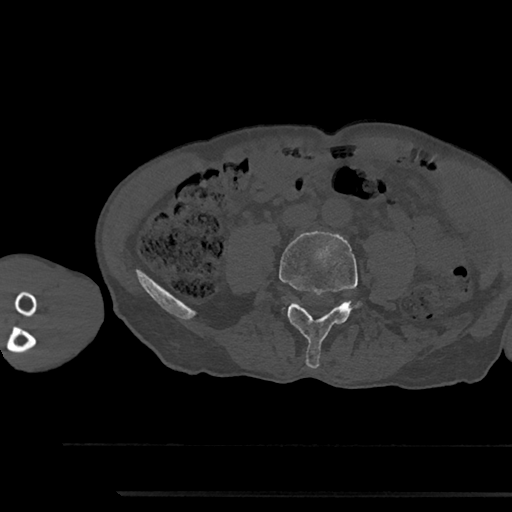
CT including the spine, one axial slice; slice 403 of 797 in the series (ordered by position); bone window (W 1800 / L 400 HU); 0.5 mm slice thickness; 512 × 512 image matrix, field of view 367 × 367 mm. Male patient, age 79 years. Case-level facts recorded for this patient, not image findings: primary cancer: prostate.
Structures marked on this image (semi-automatically segmented with operator editing):
- L4 vertebra: box from (x=279, y=231) to (x=358, y=369) px